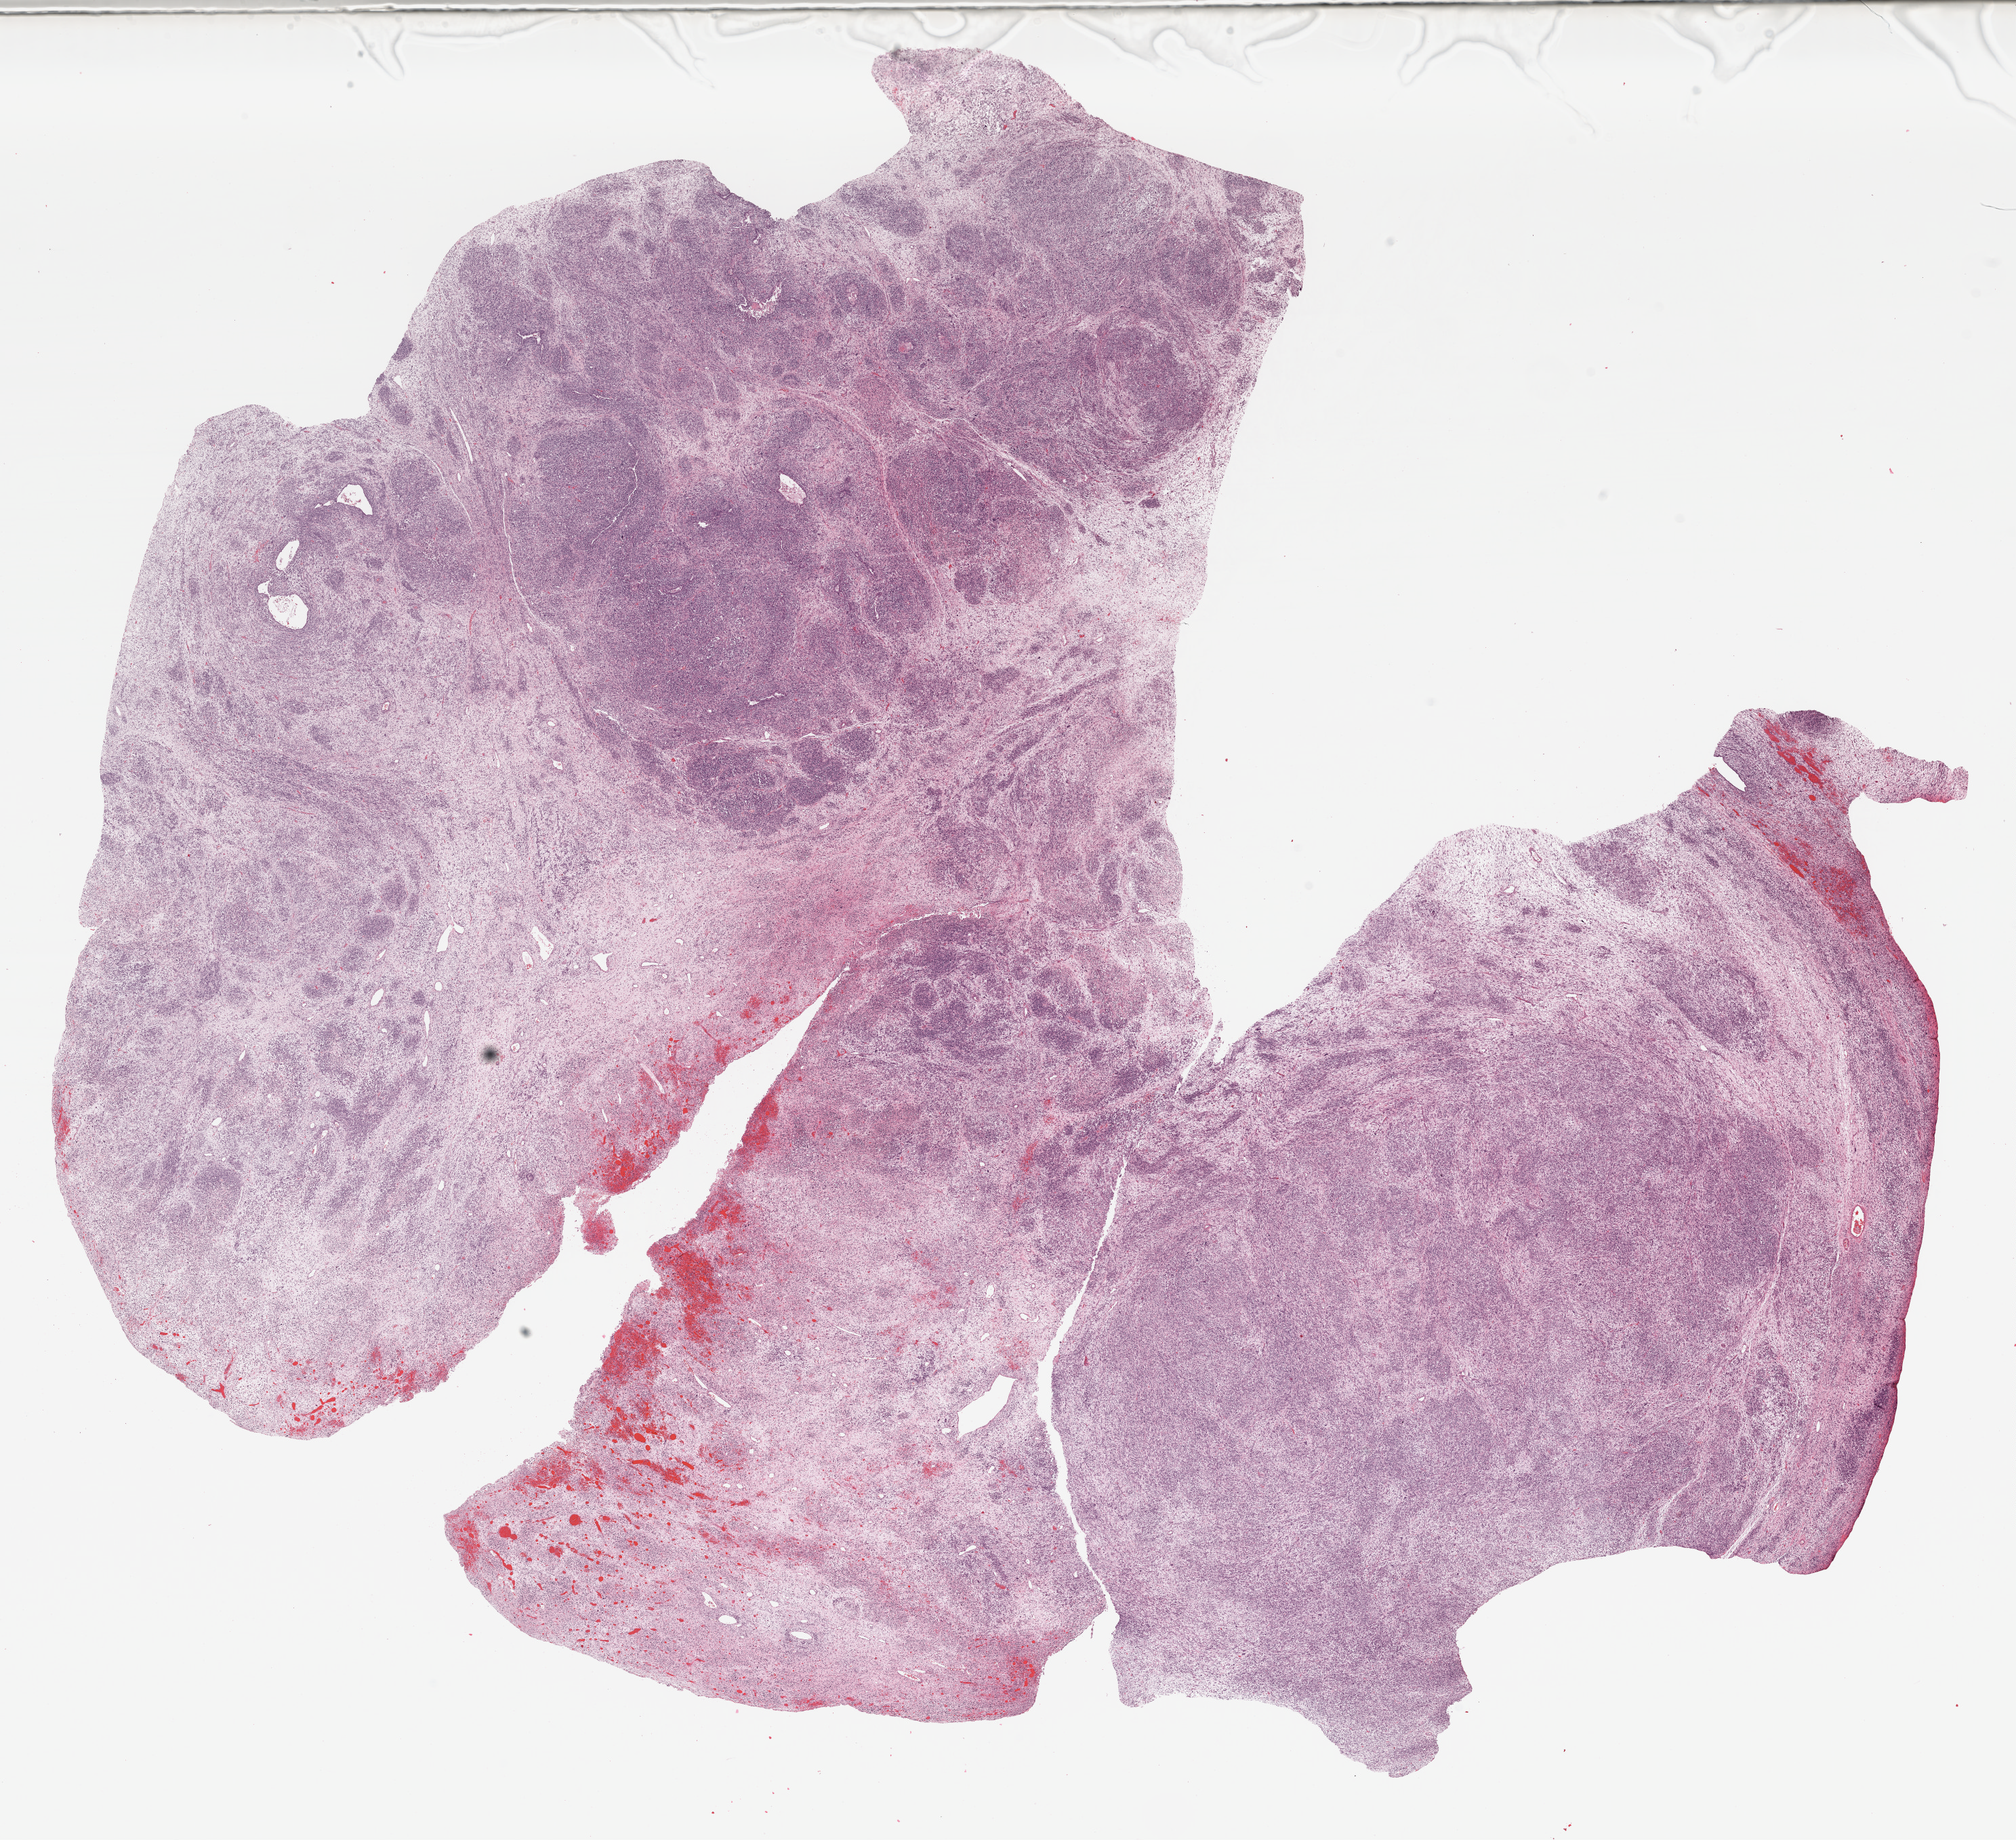
H&E whole-slide image — low-resolution overview of the scanned area, about 23.5 x 21.4 mm. FFPE section. Uterus, primary tumour sample. Female, age 68 years at initial diagnosis.
Pathologic diagnosis: Carcinosarcoma, NOS. FIGO stage: IIIC1.